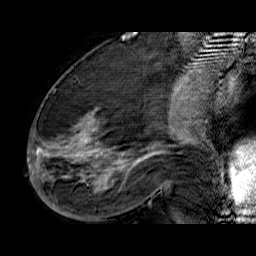
Breast MRI (dynamic contrast-enhanced), one sagittal slice; dynamic contrast-enhanced series, time point 2 of 6 at this slice position (early post-contrast); 1.5 T; TE 6.5 ms, TR 32.9 ms; 256 × 256 image matrix, field of view 200 × 200 mm. Female patient. Case-level facts recorded for this patient, not image findings: setting: breast cancer imaged before/during neoadjuvant chemotherapy; receptor status: HR-positive, HER2-negative.
Structures marked on this image (semi-automatically segmented with operator editing):
- analysis volume of interest (the breast-tissue region the enhancement analysis was run in; not a lesion): bounding box [x1, y1, x2, y2] px = [33, 74, 176, 210]
- tumour enhancement mask (voxels above the 100 % enhancement threshold inside the analysis volume of interest): [33, 109, 166, 203]